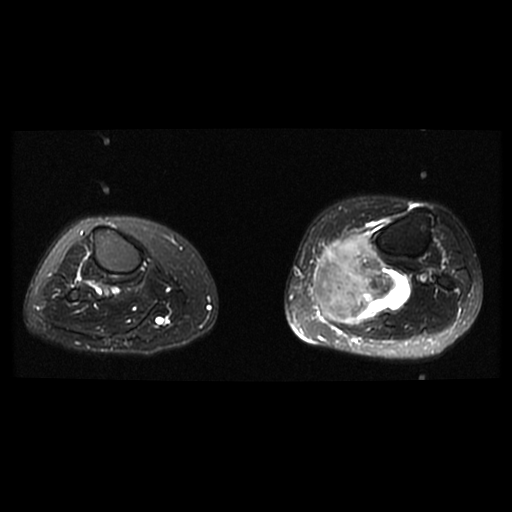
MRI of an extremity soft-tissue mass, one axial slice; slice 20 of 38 in the series (ordered by position); T2-weighted fat-saturated; 6 mm slice thickness; 512 × 512 image matrix, field of view 330 × 330 mm. Female patient. From the clinical record (not read from this slice): histological type: extraskeletal high grade osteogenic sarcoma; grade: high; site of the primary tumour: left calf.
Structures marked on this image (manually delineated by an expert):
- gross tumour volume (mass): box from (x=314, y=232) to (x=413, y=325) px